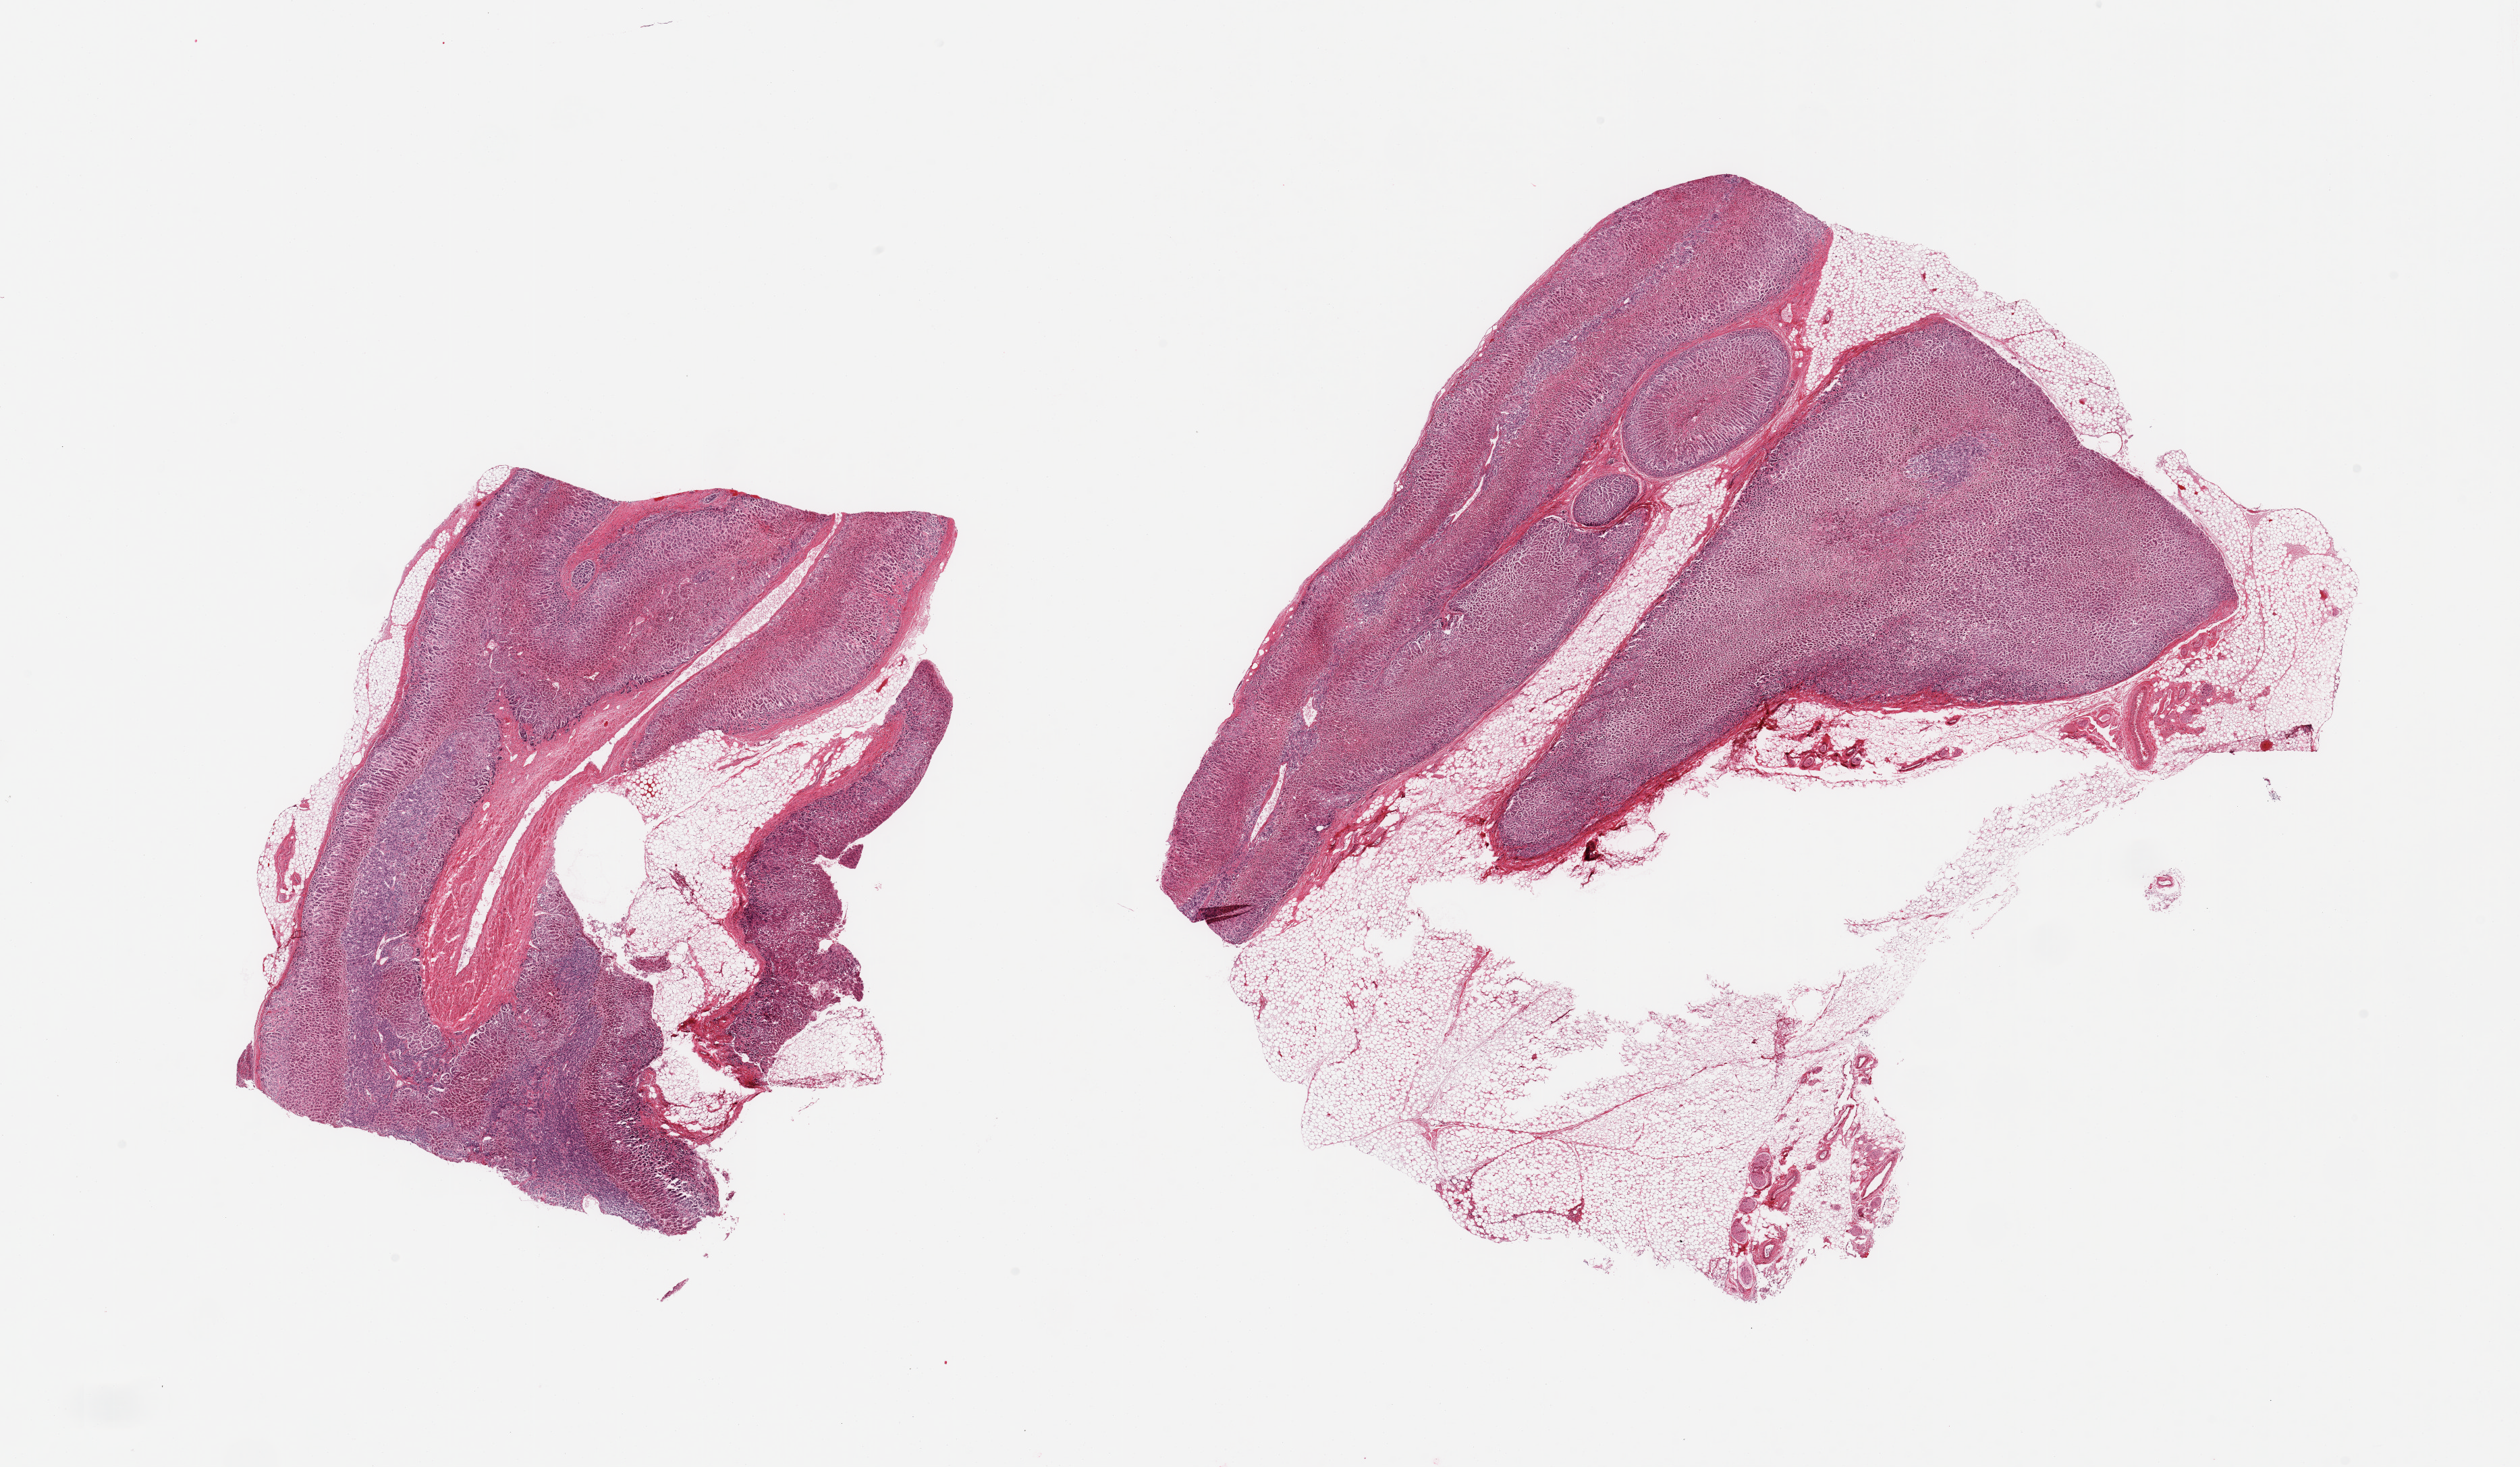
Whole-slide image, H&E stain, shown as a low-resolution overview of the whole scanned area (about 29.5 x 17.2 mm, acquisition: 20x scan); PAXgene-fixed paraffin-embedded (PFPE) section; sampled site (target tissue): adrenal gland; donor tissue sample. Female donor.
* review note (as recorded): 1 piece; adrenal with 30-40% attached fat